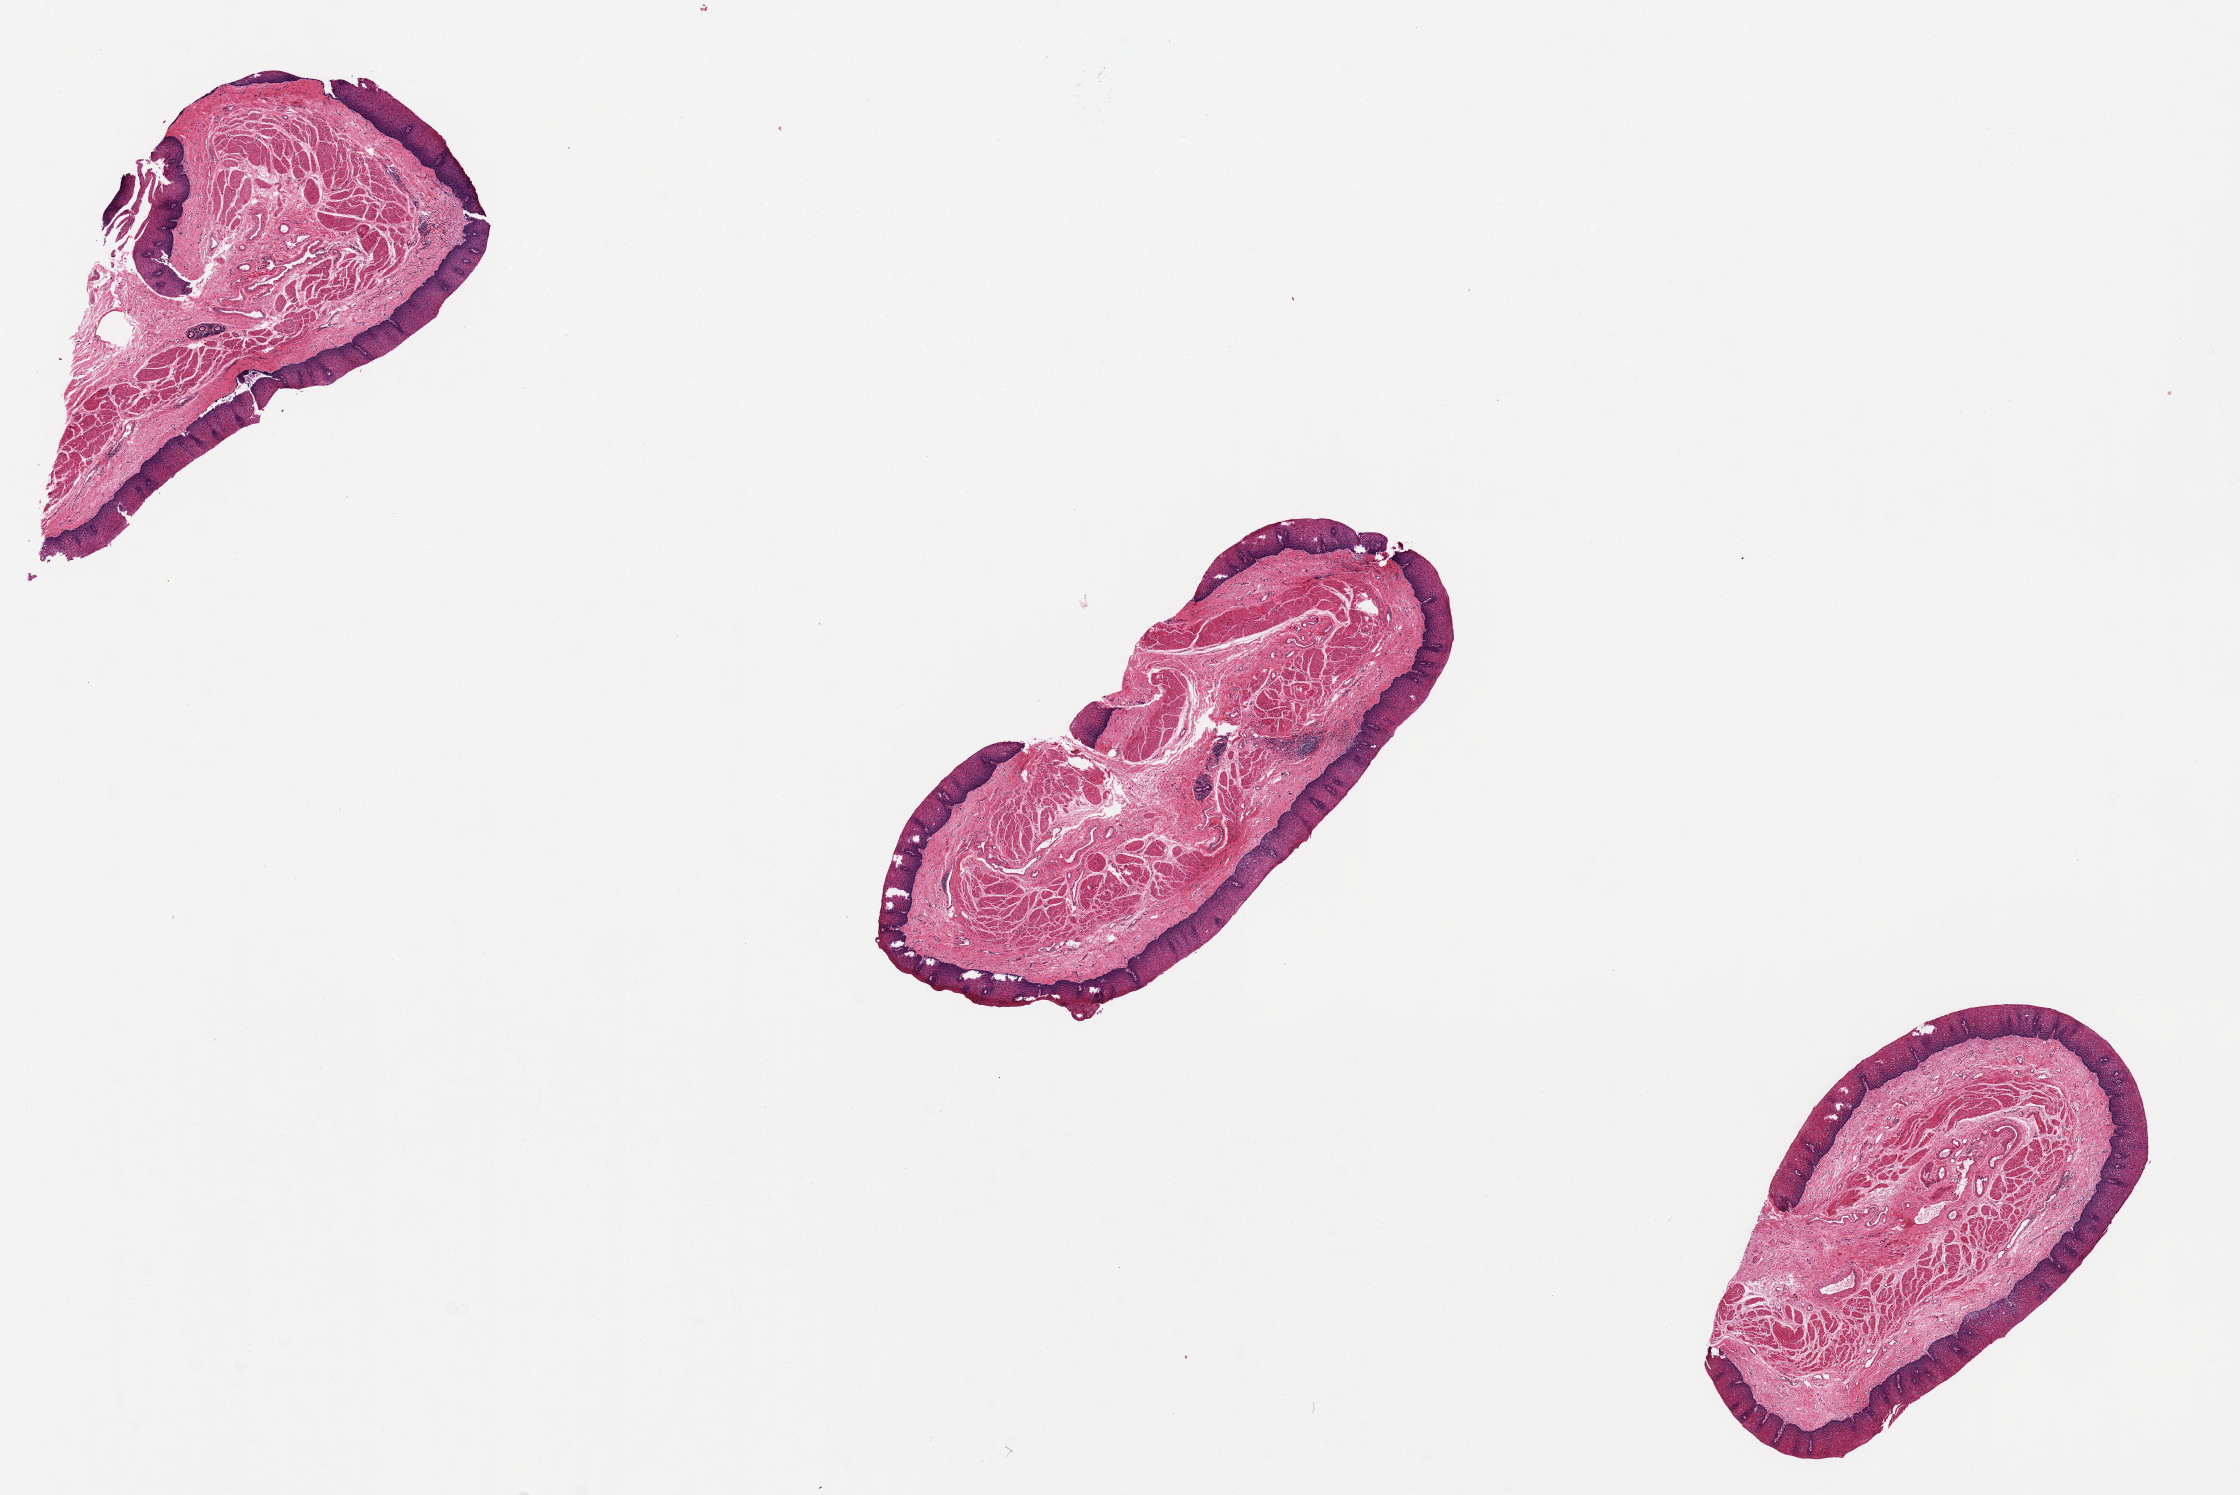
Whole-slide image, hematoxylin and eosin (H&E) stain, a low-resolution overview of the entire scanned area, about 17.7 x 11.8 mm (slide scanned at 20x), PAXgene-fixed, paraffin-embedded tissue, section of esophageal mucous membrane (target tissue), donor tissue sample. Donor: female.
Pathologist's review note for this sample: Squamous epithelium 0.2 mm thick; scattered fracture defects.